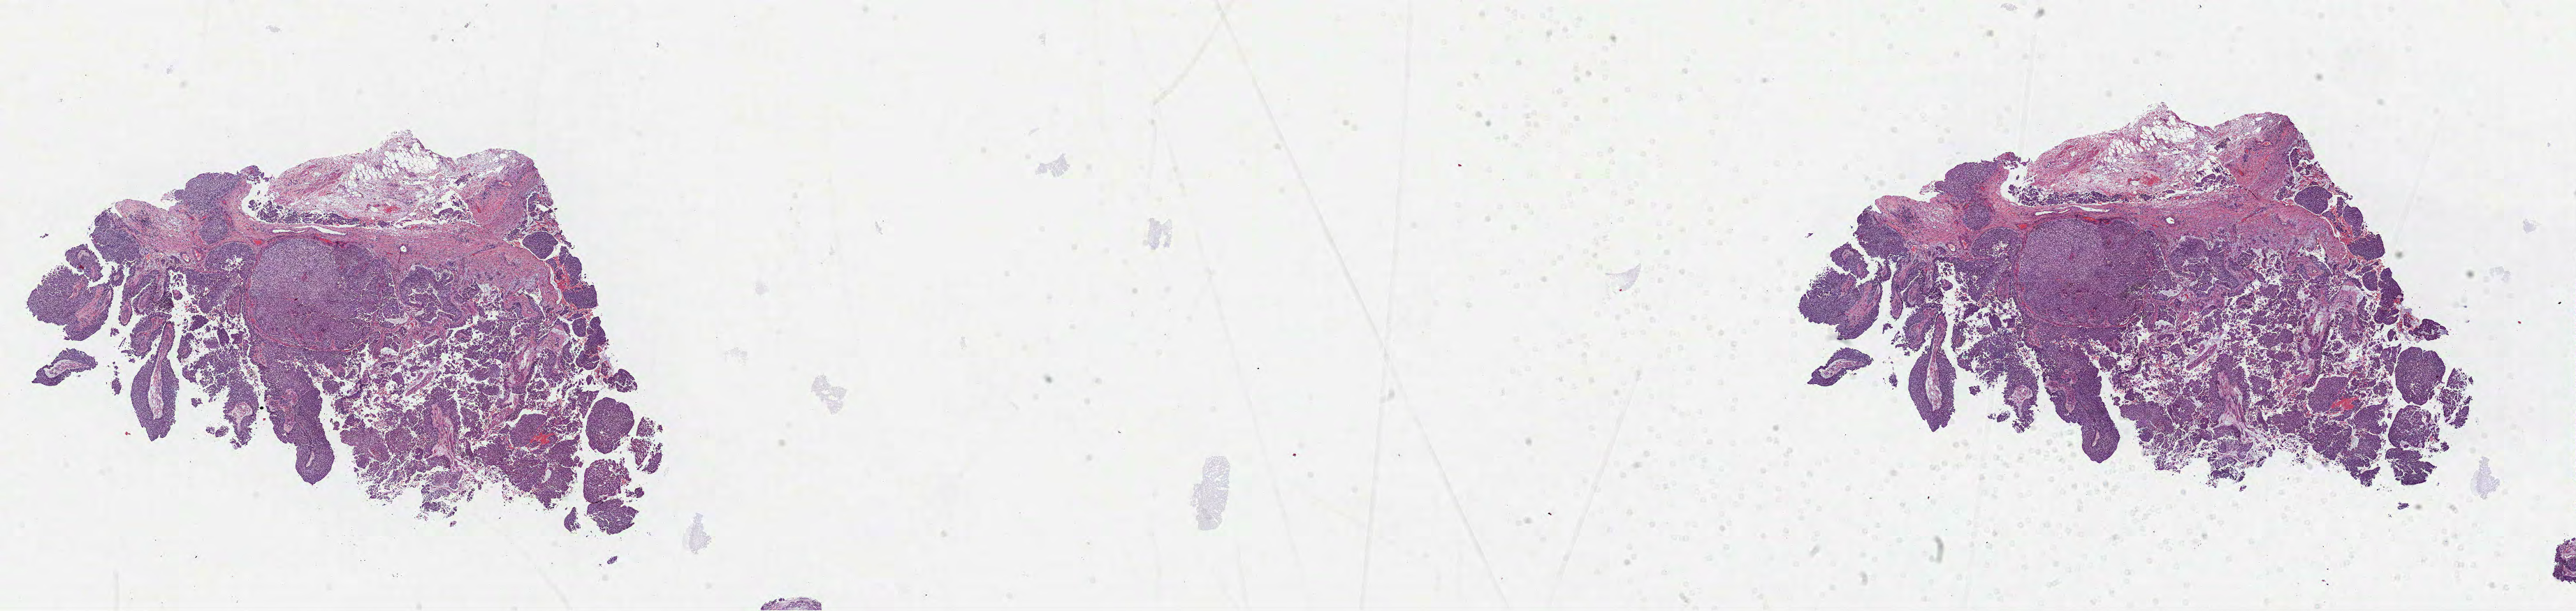
Digitized H&E-stained tissue section (whole slide) — low-resolution overview of the scanned area, about 29.7 x 7.1 mm. FFPE section. Primary tumour sample from the kidney. Male patient; age at initial diagnosis 75 years.
• laterality: right
• AJCC pathologic stage: II
• histologic diagnosis: Papillary adenocarcinoma, NOS
• TNM: T2 NX M0